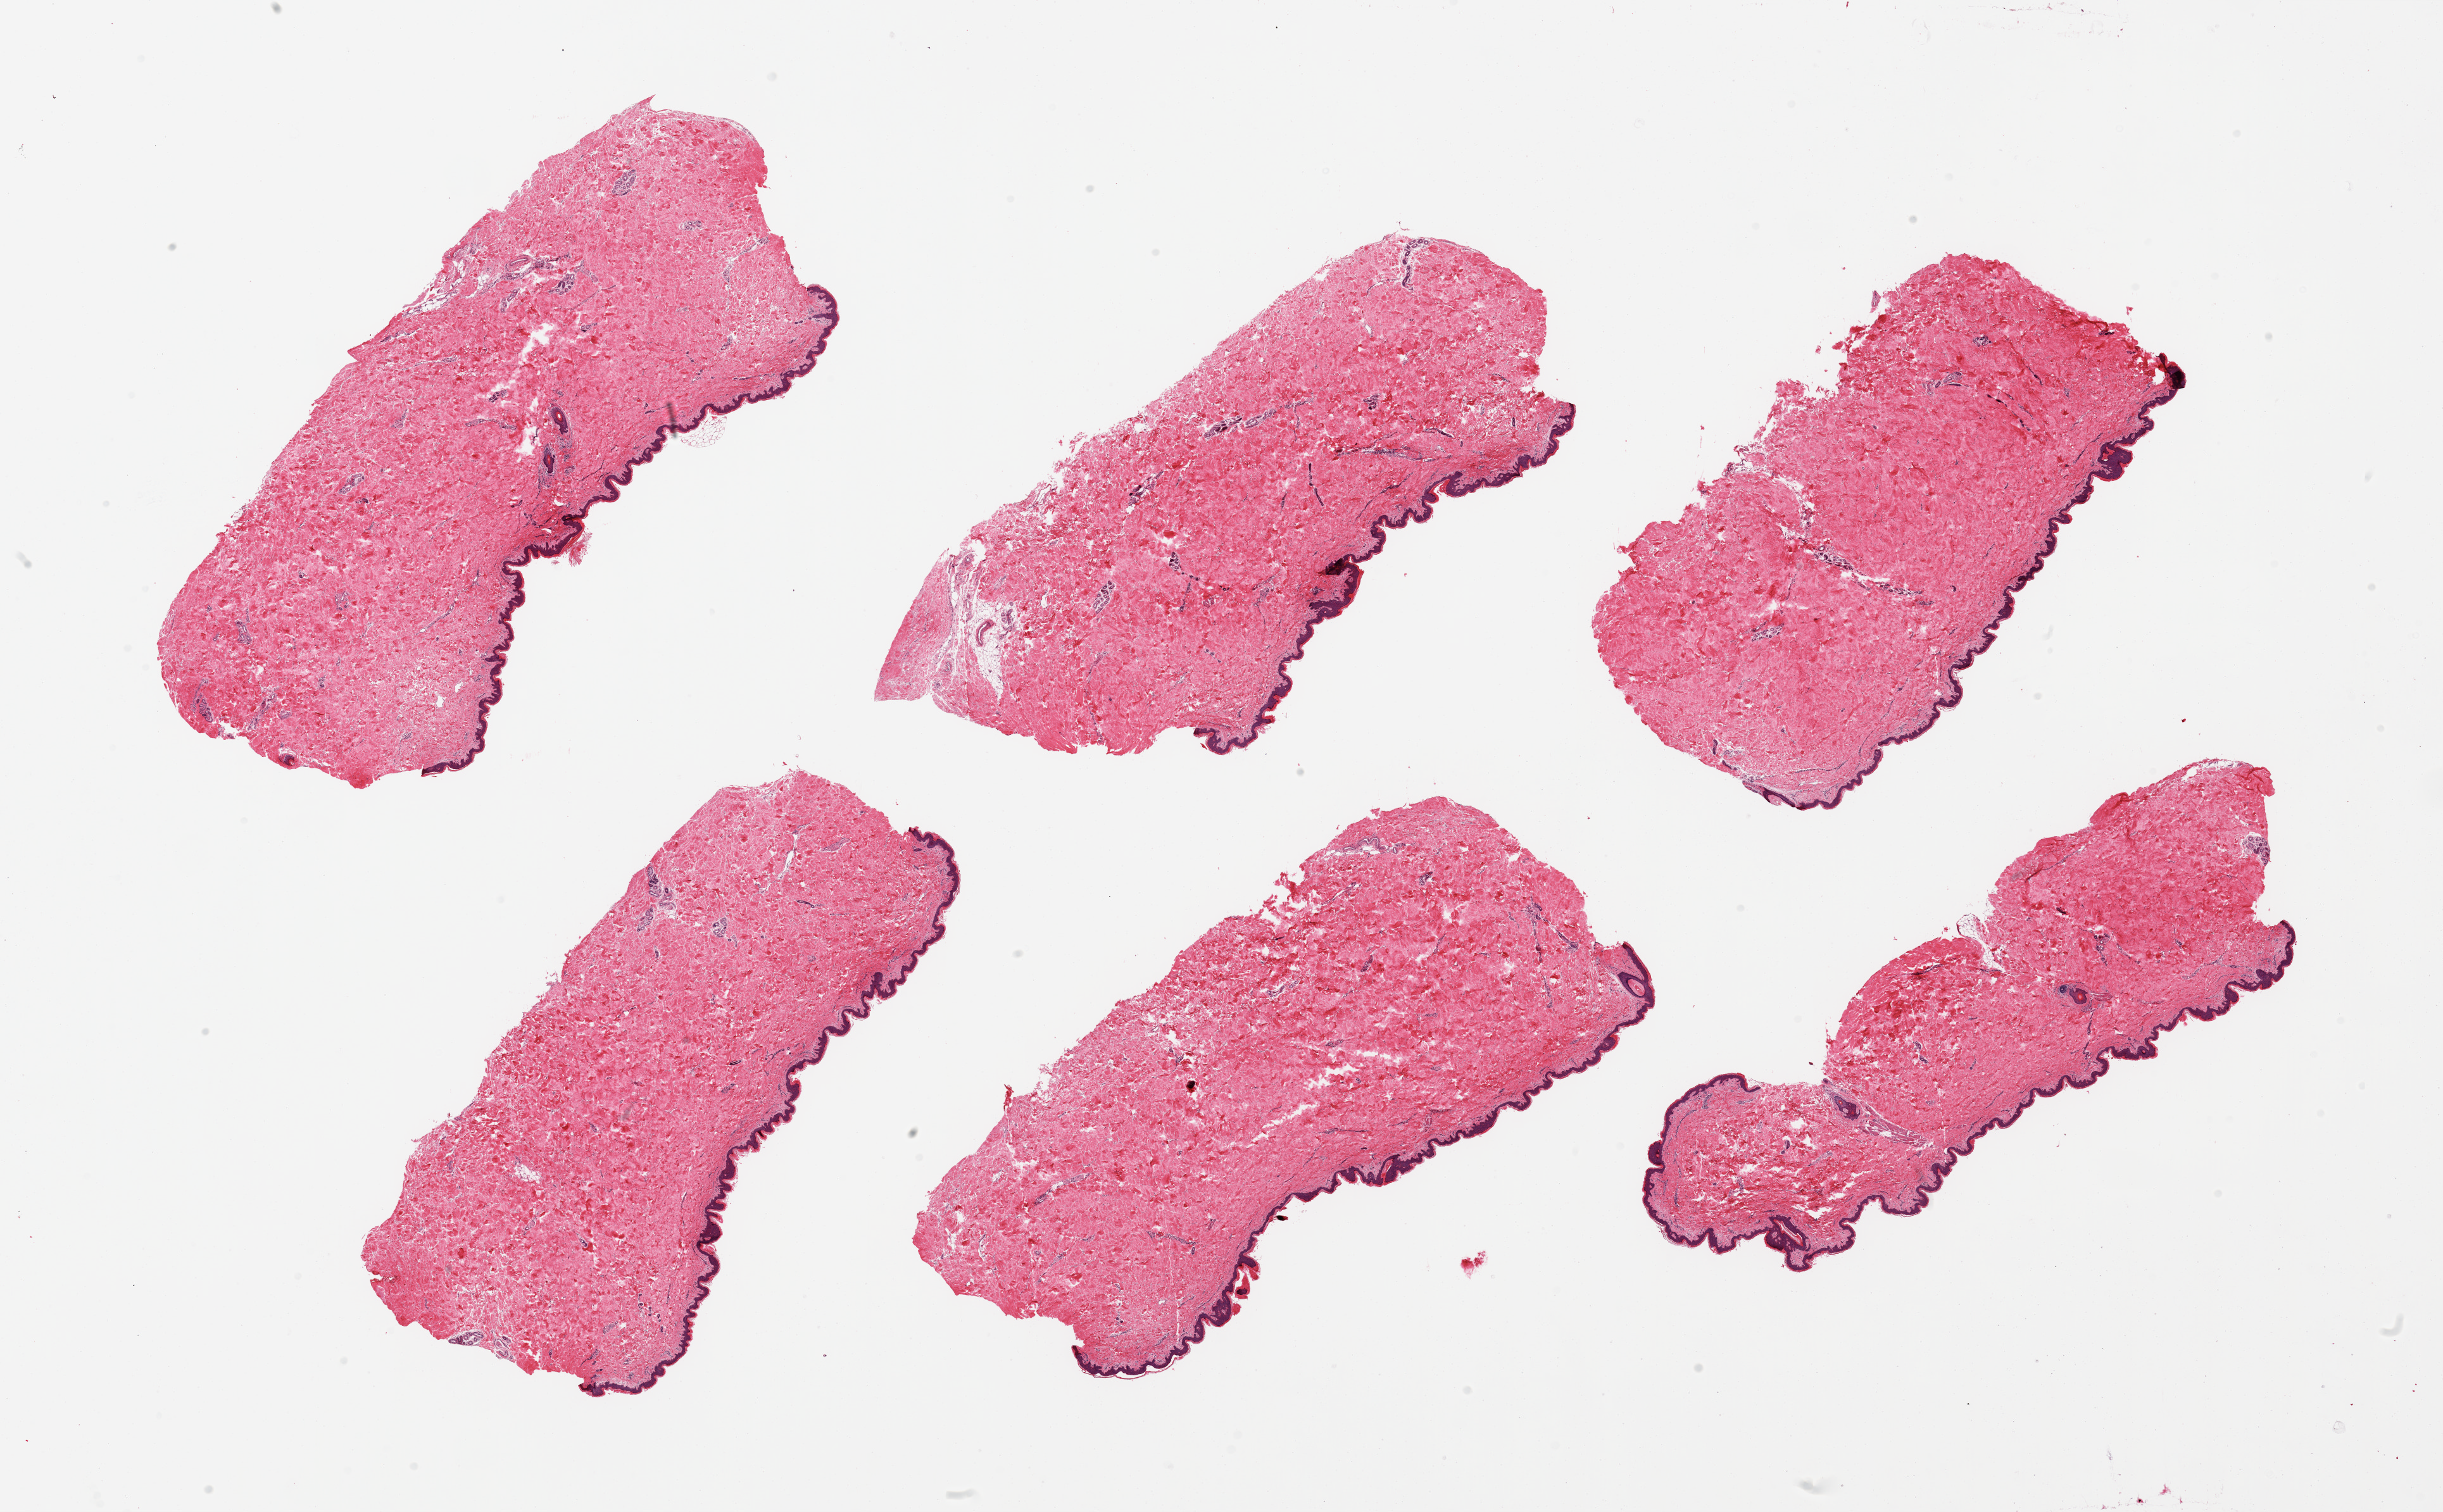
Whole-slide image, H&E stain, whole scanned area (about 30.5 x 18.9 mm, from a 20x scan) shown as a low-resolution overview. PAXgene-fixed, paraffin-embedded tissue. Sampled site (target tissue): skin of suprapubic region. Tissue donor sample. Donor sex: male.
Pathologist's review note for this sample: 6 pieces; well trimmed.